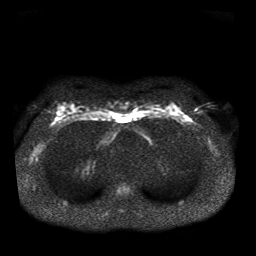
Breast MRI, one axial slice. Slice 21 of 41 in the series (ordered by position). Diffusion-weighted series; image 2 of 4 stored at this slice position (different b-values; order by instance number). 1.5 T. 5 mm slice thickness. 256 × 256 image matrix, field of view 330 × 330 mm. Female patient.
Structures marked on this image (manually delineated by an expert):
- tumour on diffusion-weighted imaging: bounding box [x1, y1, x2, y2] px = [185, 117, 191, 121]